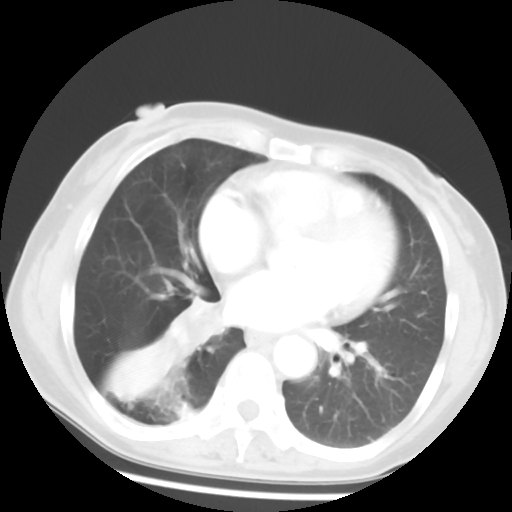
Chest CT, one axial slice; slice 24 of 52 in the series (ordered by position); reconstruction kernel STANDARD; 120 kVp; lung window (W 1500 / L -600 HU); 5 mm slice thickness; 512 × 512 image matrix, field of view 297 × 297 mm. Patient: female, 54 years. From the clinical record (not read from this slice): clinical TNM (as recorded): T1c N0 M0.
Structures marked on this image (bounding box drawn by a radiologist):
- lung tumour (recorded histology: squamous cell carcinoma): bounding box [x1, y1, x2, y2] px = [173, 293, 231, 352]